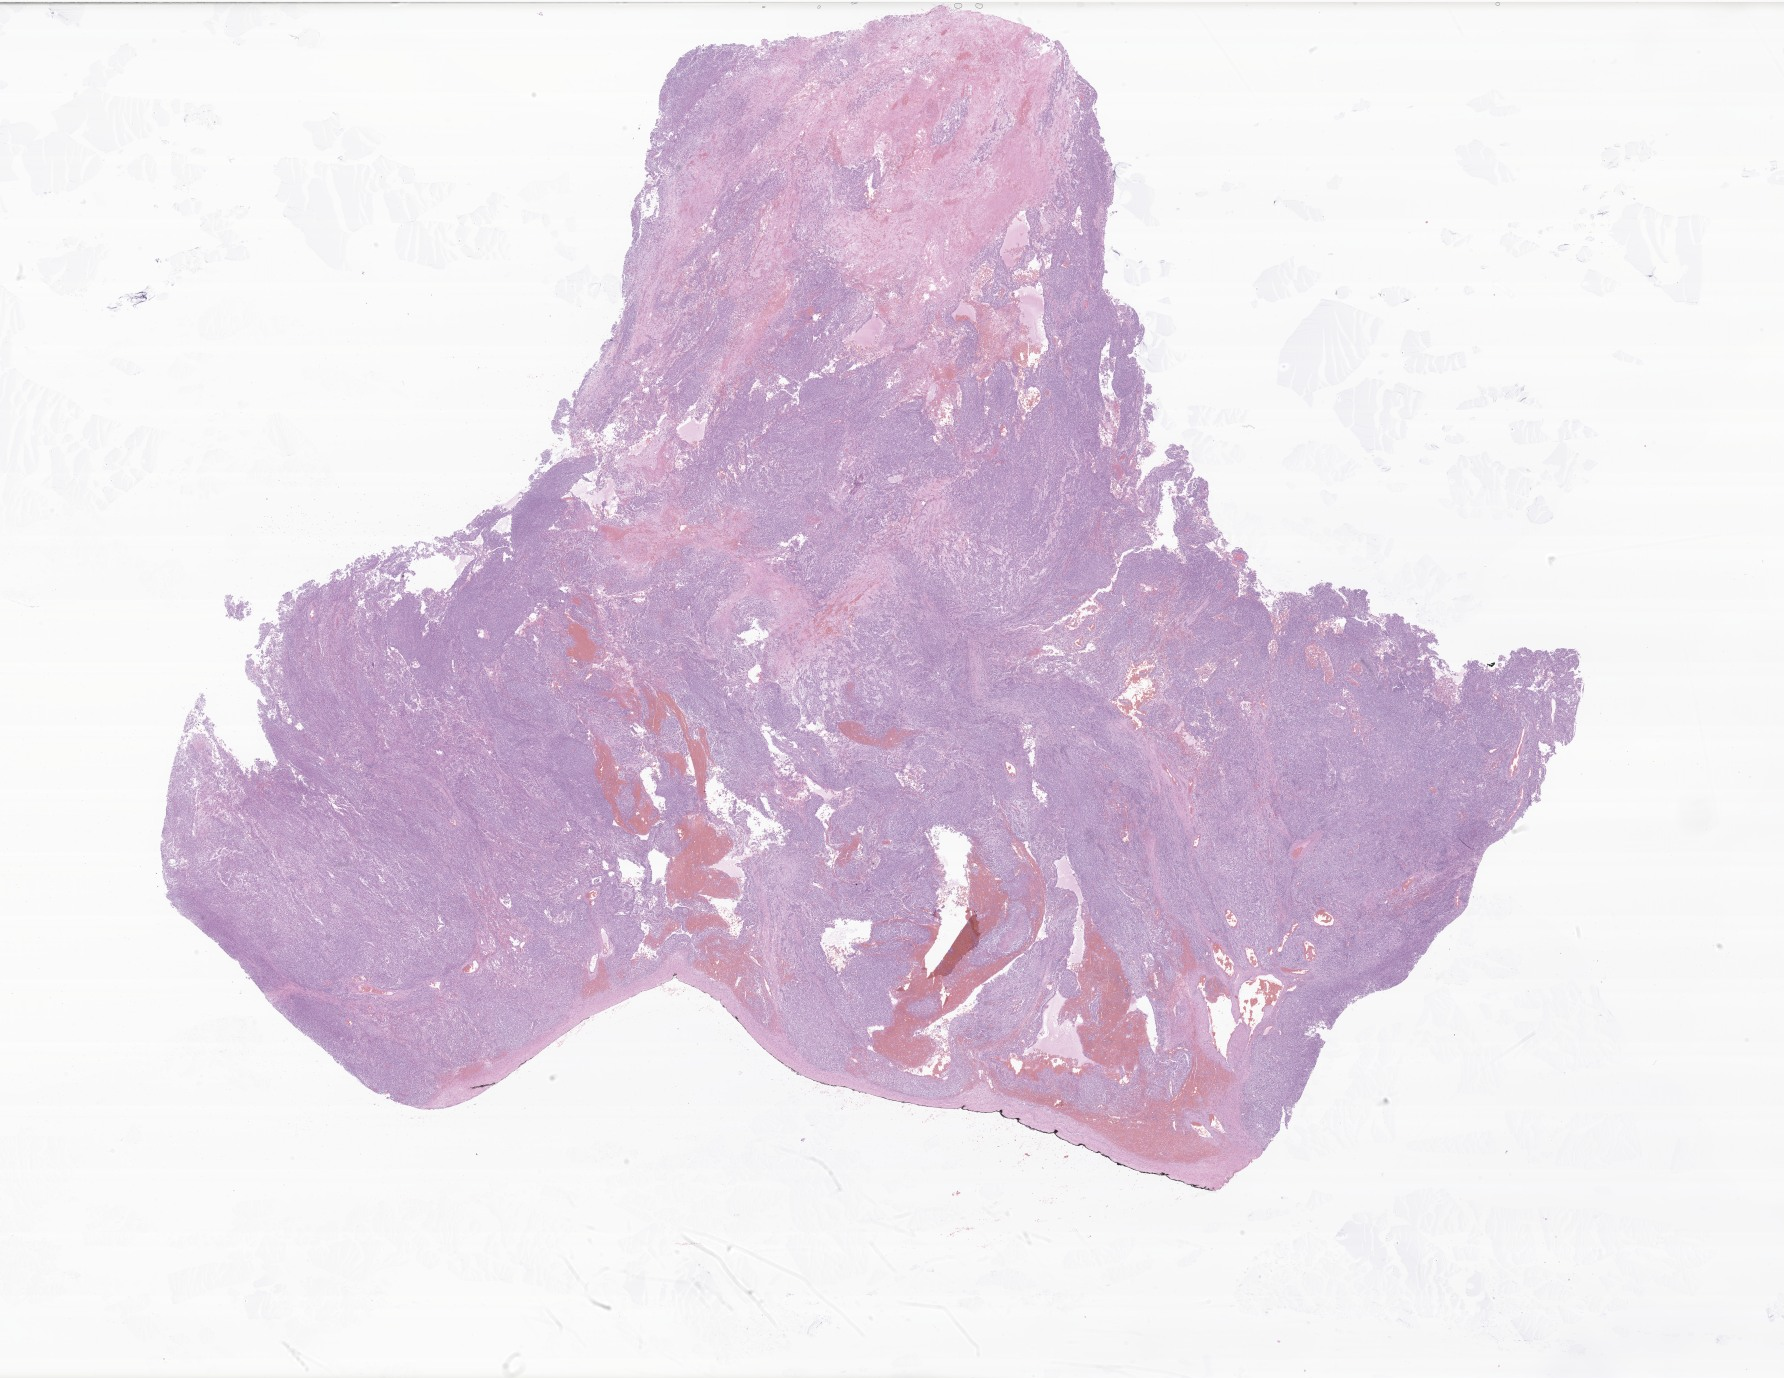
Whole-slide image, hematoxylin and eosin (H&E) stain of tumor tissue from the ovary, a low-resolution overview of the entire scanned area, about 30.1 x 23.2 mm. FFPE section. Female patient, age 190 months.
Recorded diagnosis: Small cell carcinoma, NOS.